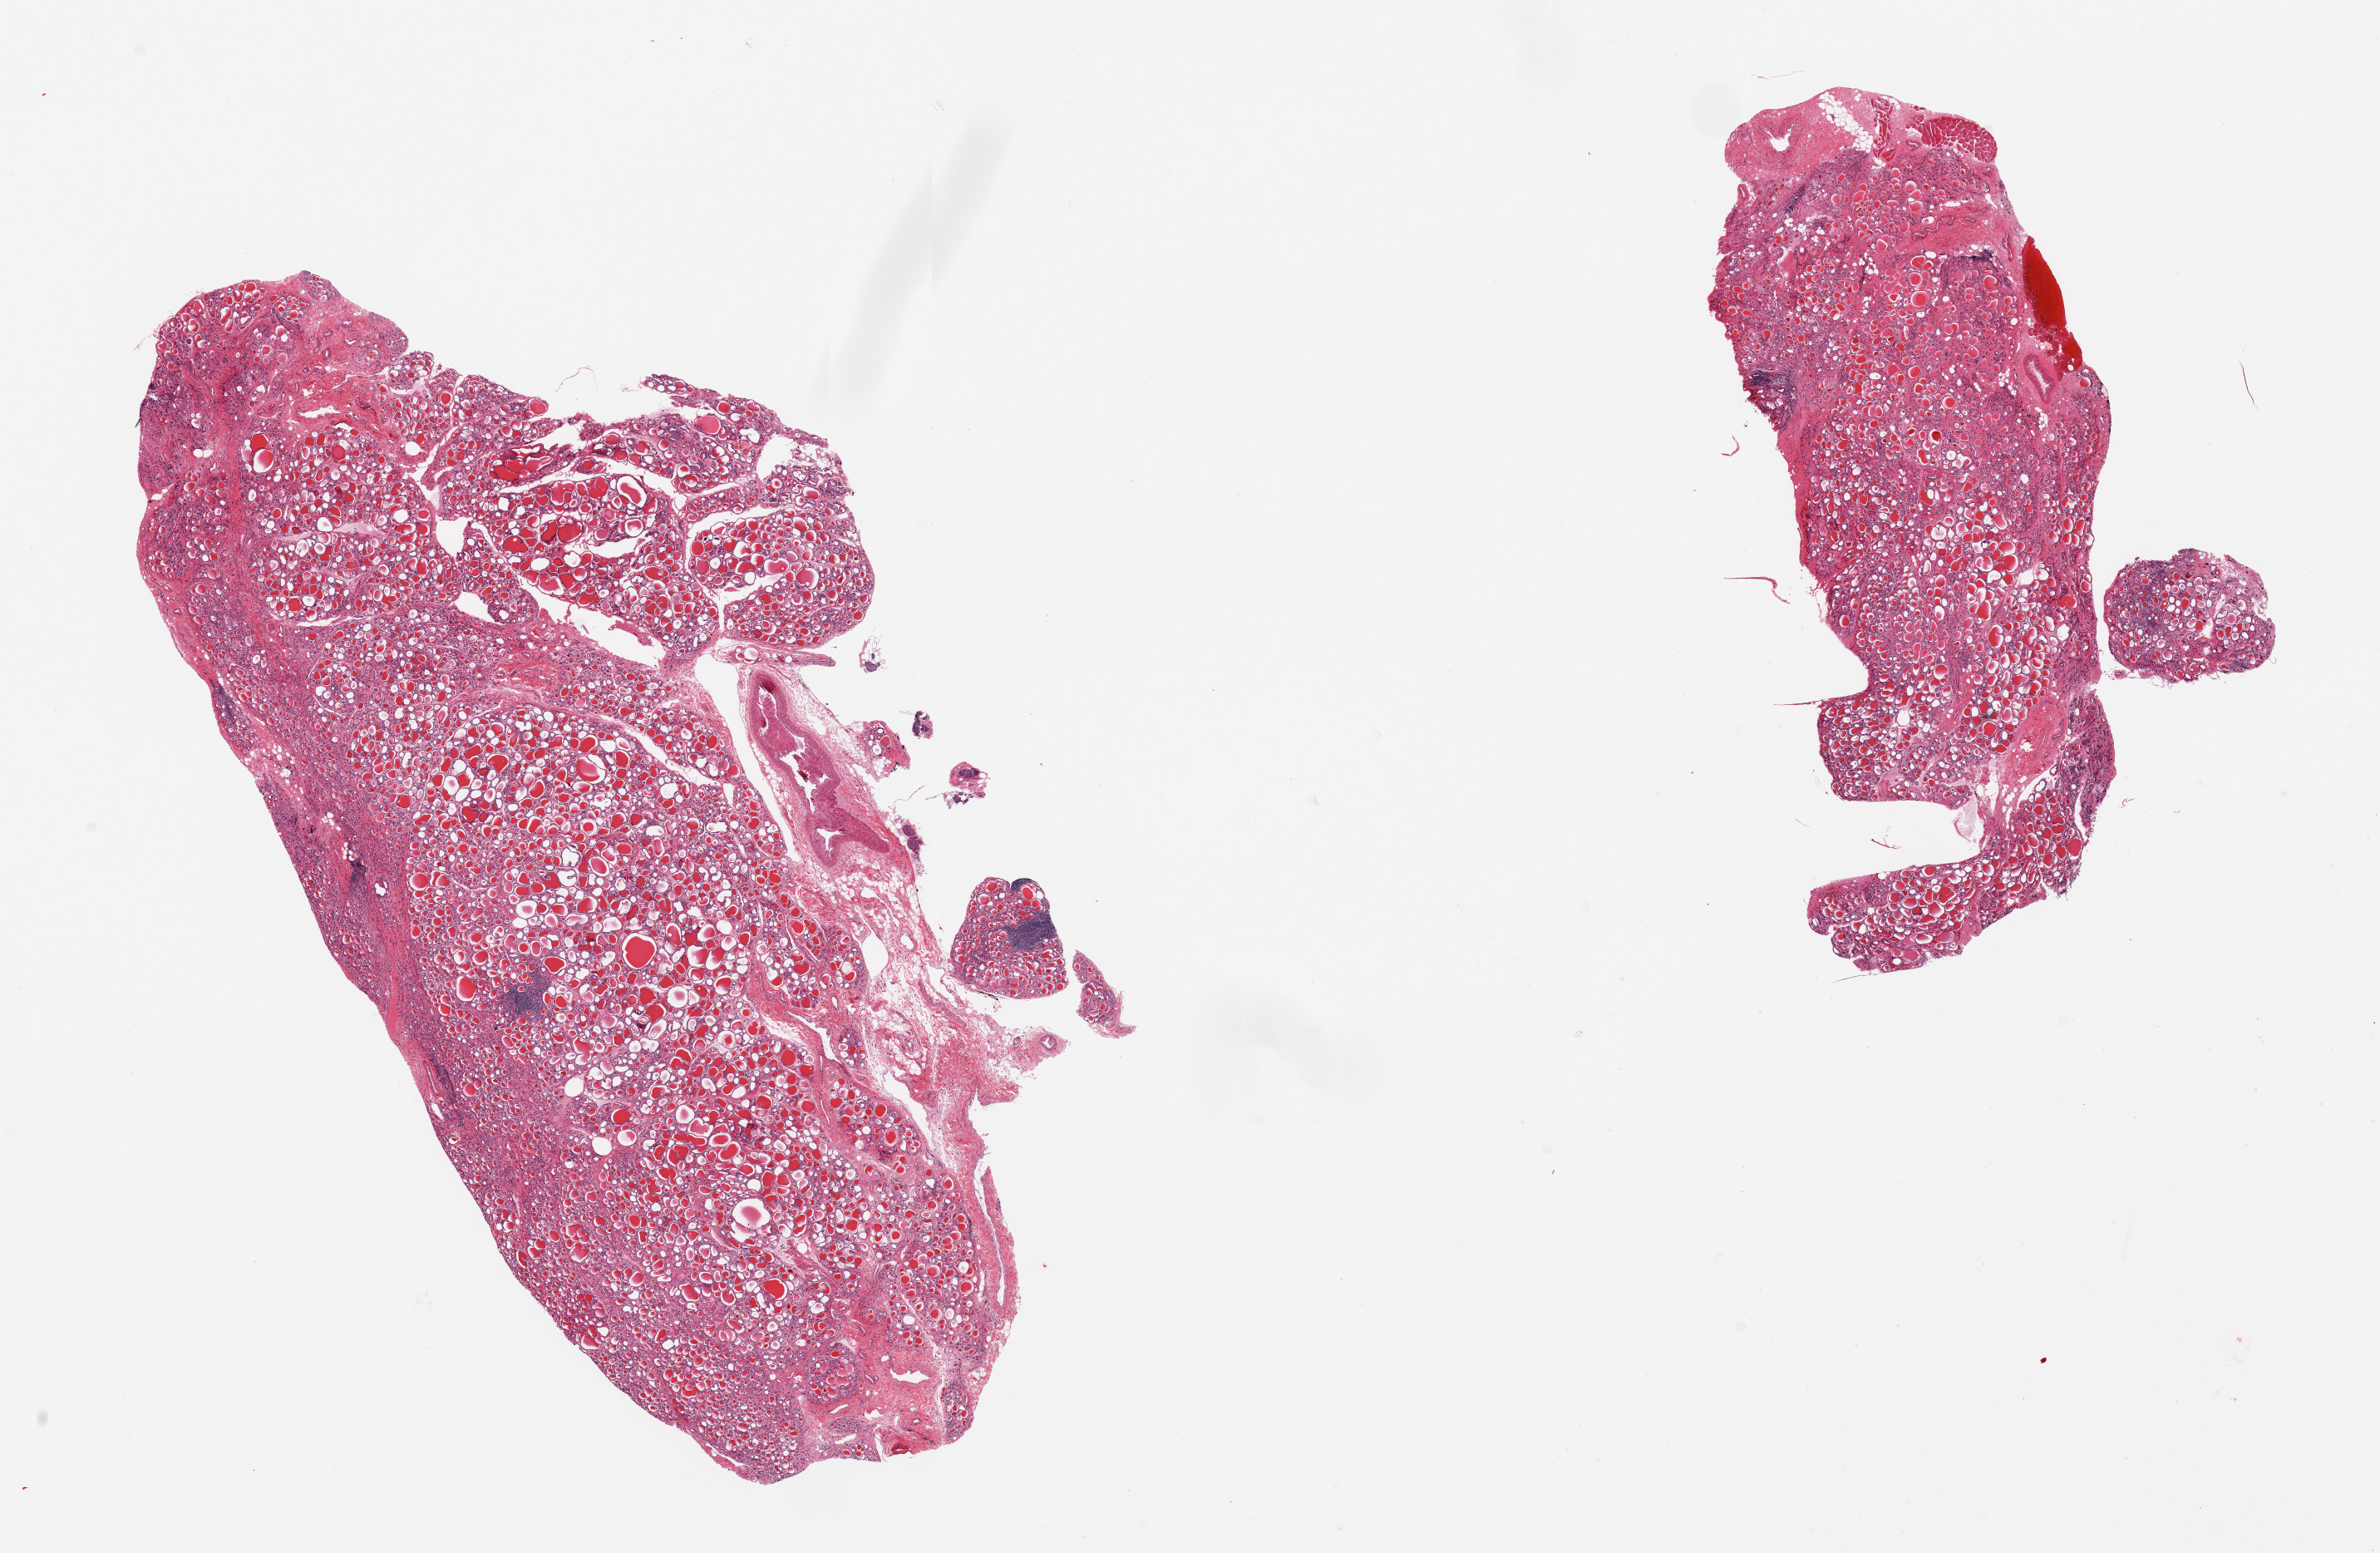
Haematoxylin and eosin whole-slide image, brightfield — shown as a low-resolution overview of the whole scanned area (about 22.6 x 14.8 mm, acquisition: 20x scan); PAXgene-fixed, paraffin-embedded tissue; section of thyroid (target tissue); tissue donor sample. Donor sex: female.
Pathologist's review note for this sample: 2 pieces, nodular goitre.